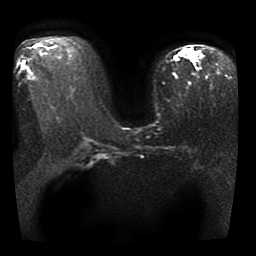
Breast MRI, one axial slice. Position 19 of 41 along the scan axis. Diffusion-weighted series; image 2 of 4 stored at this slice position (different b-values; order by instance number). 1.5 T. 256 × 256 image matrix, field of view 330 × 330 mm. Female patient.
Outlined on this slice (expert manual segmentation):
- tumour on diffusion-weighted imaging: bounding box [x1, y1, x2, y2] px = [186, 51, 194, 59]